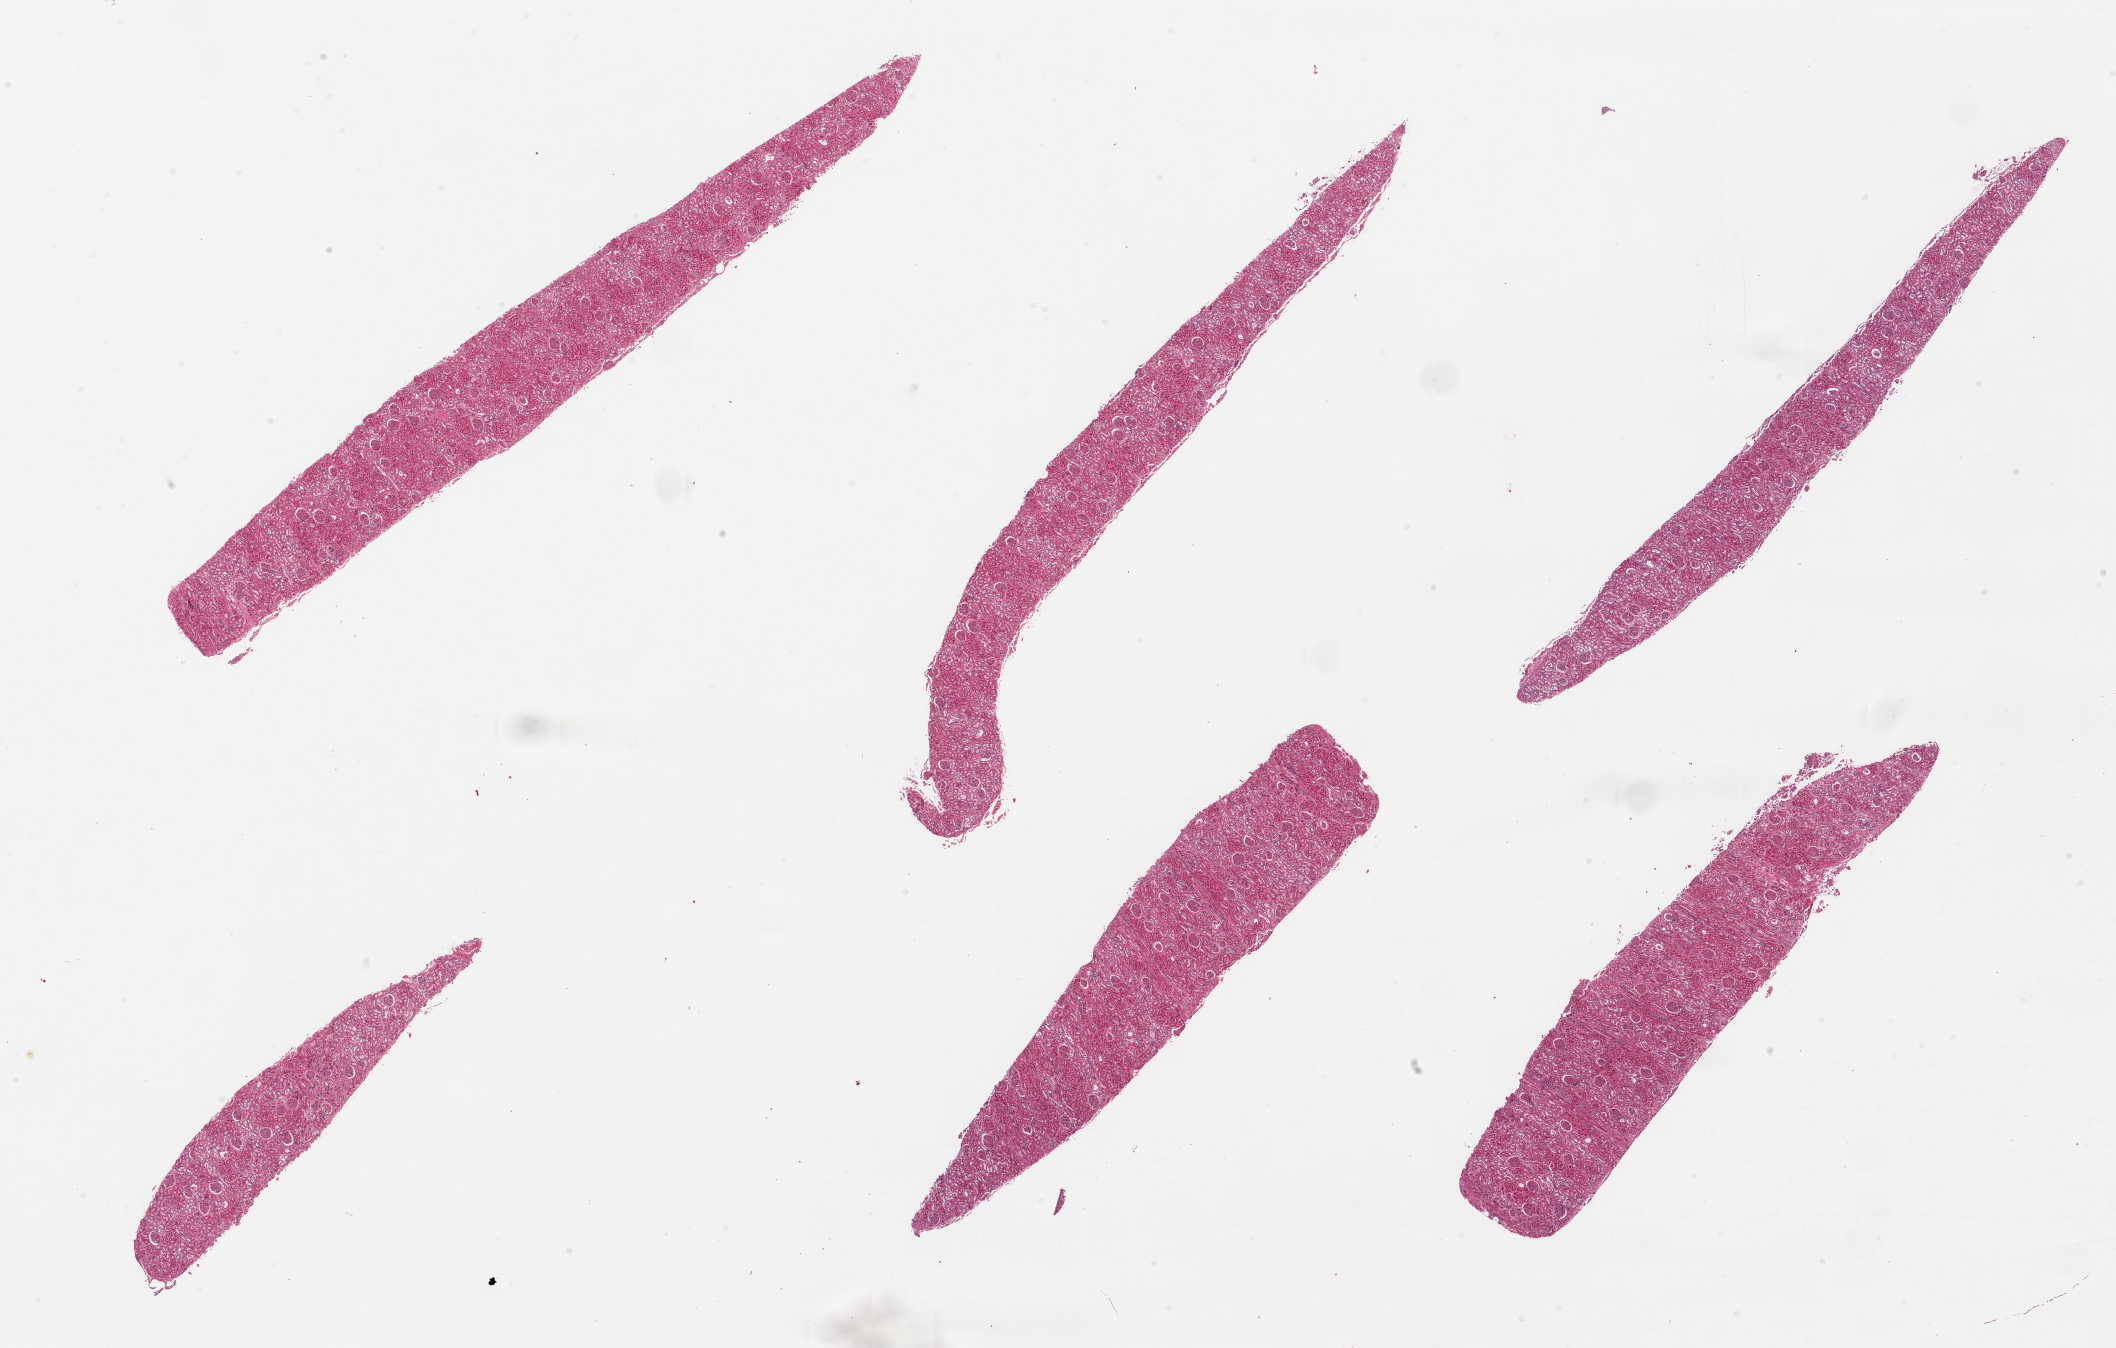
Hematoxylin and eosin (H&E) whole-slide image — whole scanned area (about 33.5 x 21.3 mm) shown as a low-resolution overview. PAXgene-fixed paraffin-embedded (PFPE) section. Sampled site (target tissue): renal cortex. Tissue donor sample. Donor: male.
Reviewer comment on this tissue sample: 6 pieces, glomeruli present, tubules autolyzed.